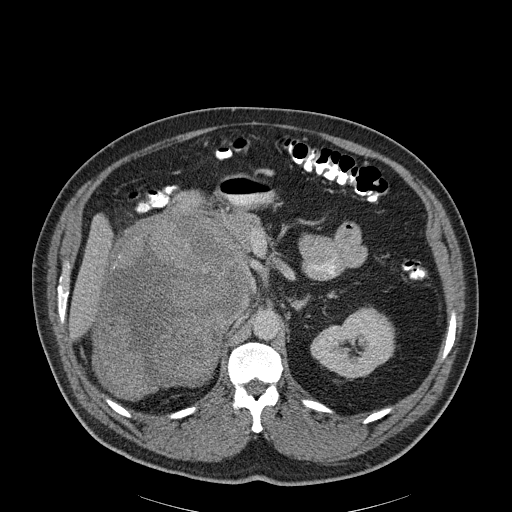
Contrast-enhanced abdominal CT, one axial slice; reconstruction kernel B30f; 120 kVp; soft-tissue window (W 400 / L 40 HU); 3 mm slice thickness; 512 × 512 image matrix, field of view 464 × 464 mm. Patient: male, 56 years. Case-level facts recorded for this patient, not image findings: diagnosis: adrenocortical carcinoma; tumour side: right adrenal.
Outlined on this slice (semi-automatic segmentation, software-assisted and operator-edited):
- mass: bounding box (x1, y1, x2, y2) in pixels: (98, 216, 248, 401)